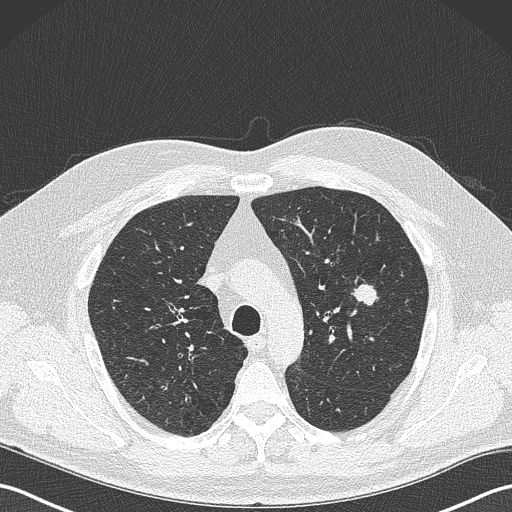
Axial slice from a low-dose chest CT screening exam; first (baseline) screen; lung window (W 1500 / L -600 HU); 1 mm slice thickness; slice 97 of 343 in the series; 512 × 512 image matrix. Male, age 61 years at enrolment.
Expert-annotated lung lesion, bounding box [x1, y1, x2, y2] px = [343, 277, 385, 316]. The screening reader recorded 2 non-calcified nodules or masses ≥4 mm on this exam (left upper lobe, lingula); which of them this box marks is not recorded. Later outcome: lung cancer diagnosed 160 days after this screen — adenocarcinoma, NOS, left upper lobe, poorly differentiated (G3), stage IA (AJCC 6th edition), 28 mm at pathology.